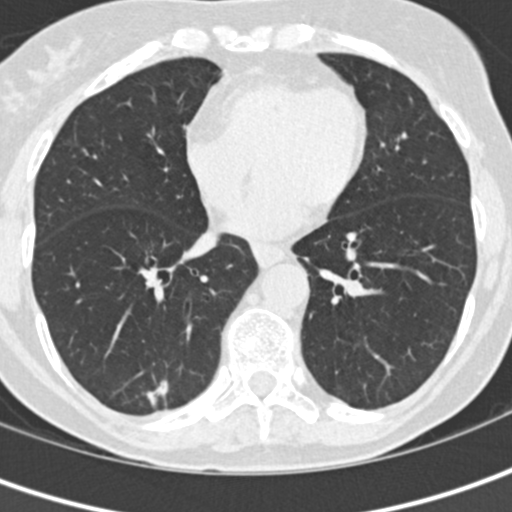
Low-dose screening chest CT, one axial slice. Slice 60 of 152 in the series (ordered by position). Reconstruction kernel B30f. 120 kVp. Lung window (W 1500 / L -600 HU). 2 mm slice thickness. 512 × 512 image matrix, field of view 280 × 280 mm.
Structures marked on this image (manually delineated by an expert):
- lesion 1 (tumor, lower lobe of right lung): box from (x=146, y=380) to (x=168, y=407) px